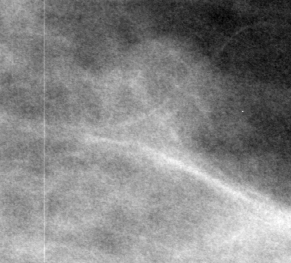
Region of interest cut from a scanned film mammogram (one marked finding); left breast; CC view; BI-RADS breast density category 1 (scale 1–4).
Finding: mass, shape lobulated, margins circumscribed; BI-RADS assessment category 3; pathology (as recorded): benign.